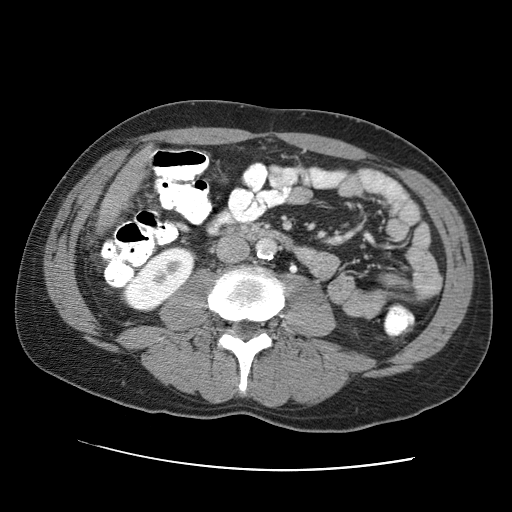
Contrast-enhanced abdominal CT (liver protocol), one axial slice. Position 6 of 95 along the scan axis. One of 2 acquisitions stored at this slice position. Soft-tissue window (W 400 / L 40 HU). 2.5 mm slice thickness. 512 × 512 image matrix. Case-level facts recorded for this patient, not image findings: diagnosis: hepatocellular carcinoma (patient treated with transarterial chemoembolisation; whether this scan precedes or follows treatment is not stated here); TNM stage (as recorded): Stage-IVA; Child-Pugh class: A; tumour nodularity: multinodular.
Outlined on this slice (semi-automatically segmented with operator editing):
- liver parenchyma outside the tumour (the mass and vessels are separate outlines, so this box may not span the whole liver): bounding box <98,148,152,230> (left, top, right, bottom; pixels)